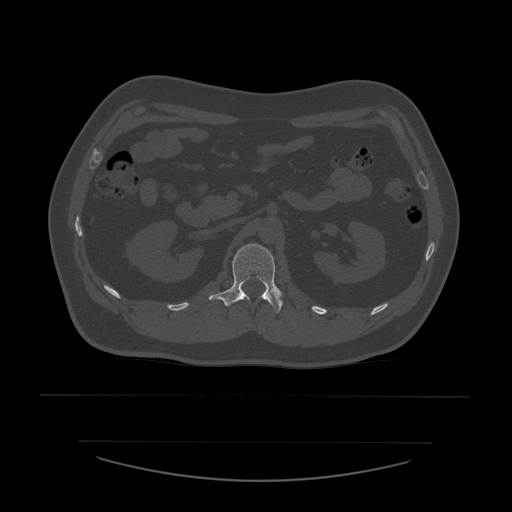
CT including the spine, one axial slice. Slice 229 of 532 in the series (ordered by position). Reconstruction kernel STANDARD. 120 kVp. Bone window (W 1800 / L 400 HU). 1.25 mm slice thickness. 512 × 512 image matrix, field of view 441 × 441 mm. Patient age 44 years. From the clinical record (not read from this slice): primary cancer: soft tissue sarcoma.
Outlined on this slice (semi-automatic segmentation, software-assisted and operator-edited):
- L1 vertebra: box from (x=209, y=244) to (x=283, y=314) px